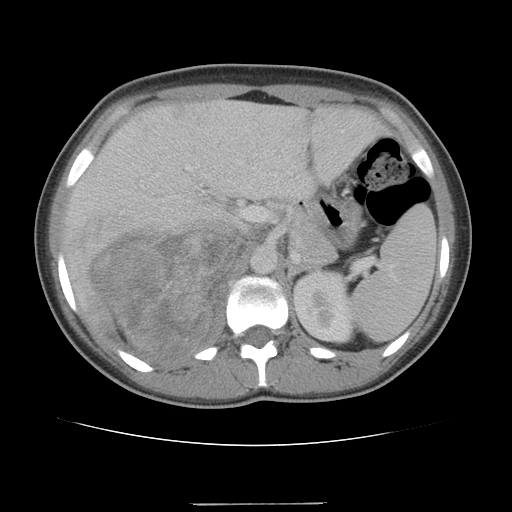
Contrast-enhanced abdominal CT, one axial slice; position 73 of 100 along the scan axis; intravenous contrast given; soft-tissue window (W 400 / L 40 HU); 5 mm slice thickness; 512 × 512 image matrix, field of view 360 × 360 mm. Female patient, age 21 years. Case-level facts recorded for this patient, not image findings: diagnosis: adrenocortical carcinoma; tumour side: right adrenal; tumour size at pathology: 15.5 cm; Ki-67 index: 26 %; stage (as recorded): 3.
Annotated regions visible in this slice (semi-automatically segmented with operator editing):
- mass: box from (x=93, y=229) to (x=247, y=363) px